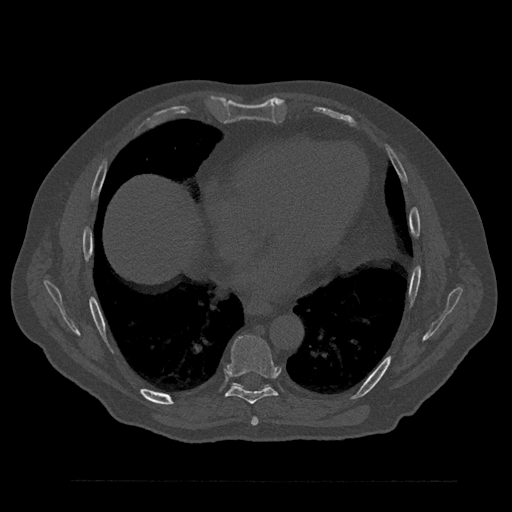
CT including the spine, one axial slice. Slice 449 of 797 in the series (ordered by position). Reconstruction kernel Br40s/3. Bone window (W 1800 / L 400 HU). 512 × 512 image matrix, field of view 430 × 430 mm. Patient: male, 61 years. Case-level facts recorded for this patient, not image findings: primary cancer: prostate.
Annotated regions visible in this slice (semi-automatically segmented with operator editing):
- T7 vertebra: bounding box [x1, y1, x2, y2] px = [251, 417, 258, 426]
- T8 vertebra: [225, 335, 278, 404]
- T9 vertebra: [236, 384, 240, 386]